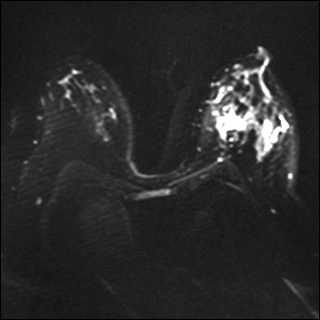
Breast MRI, one axial slice. Position 21 of 41 along the scan axis. Diffusion-weighted series; image 2 of 4 stored at this slice position (different b-values; order by instance number). 1.5 T. 4 mm slice thickness. 320 × 320 image matrix, field of view 340 × 340 mm. Female patient.
Structures marked on this image (manually delineated by an expert):
- tumour on diffusion-weighted imaging: bounding box [x1, y1, x2, y2] px = [219, 114, 251, 131]